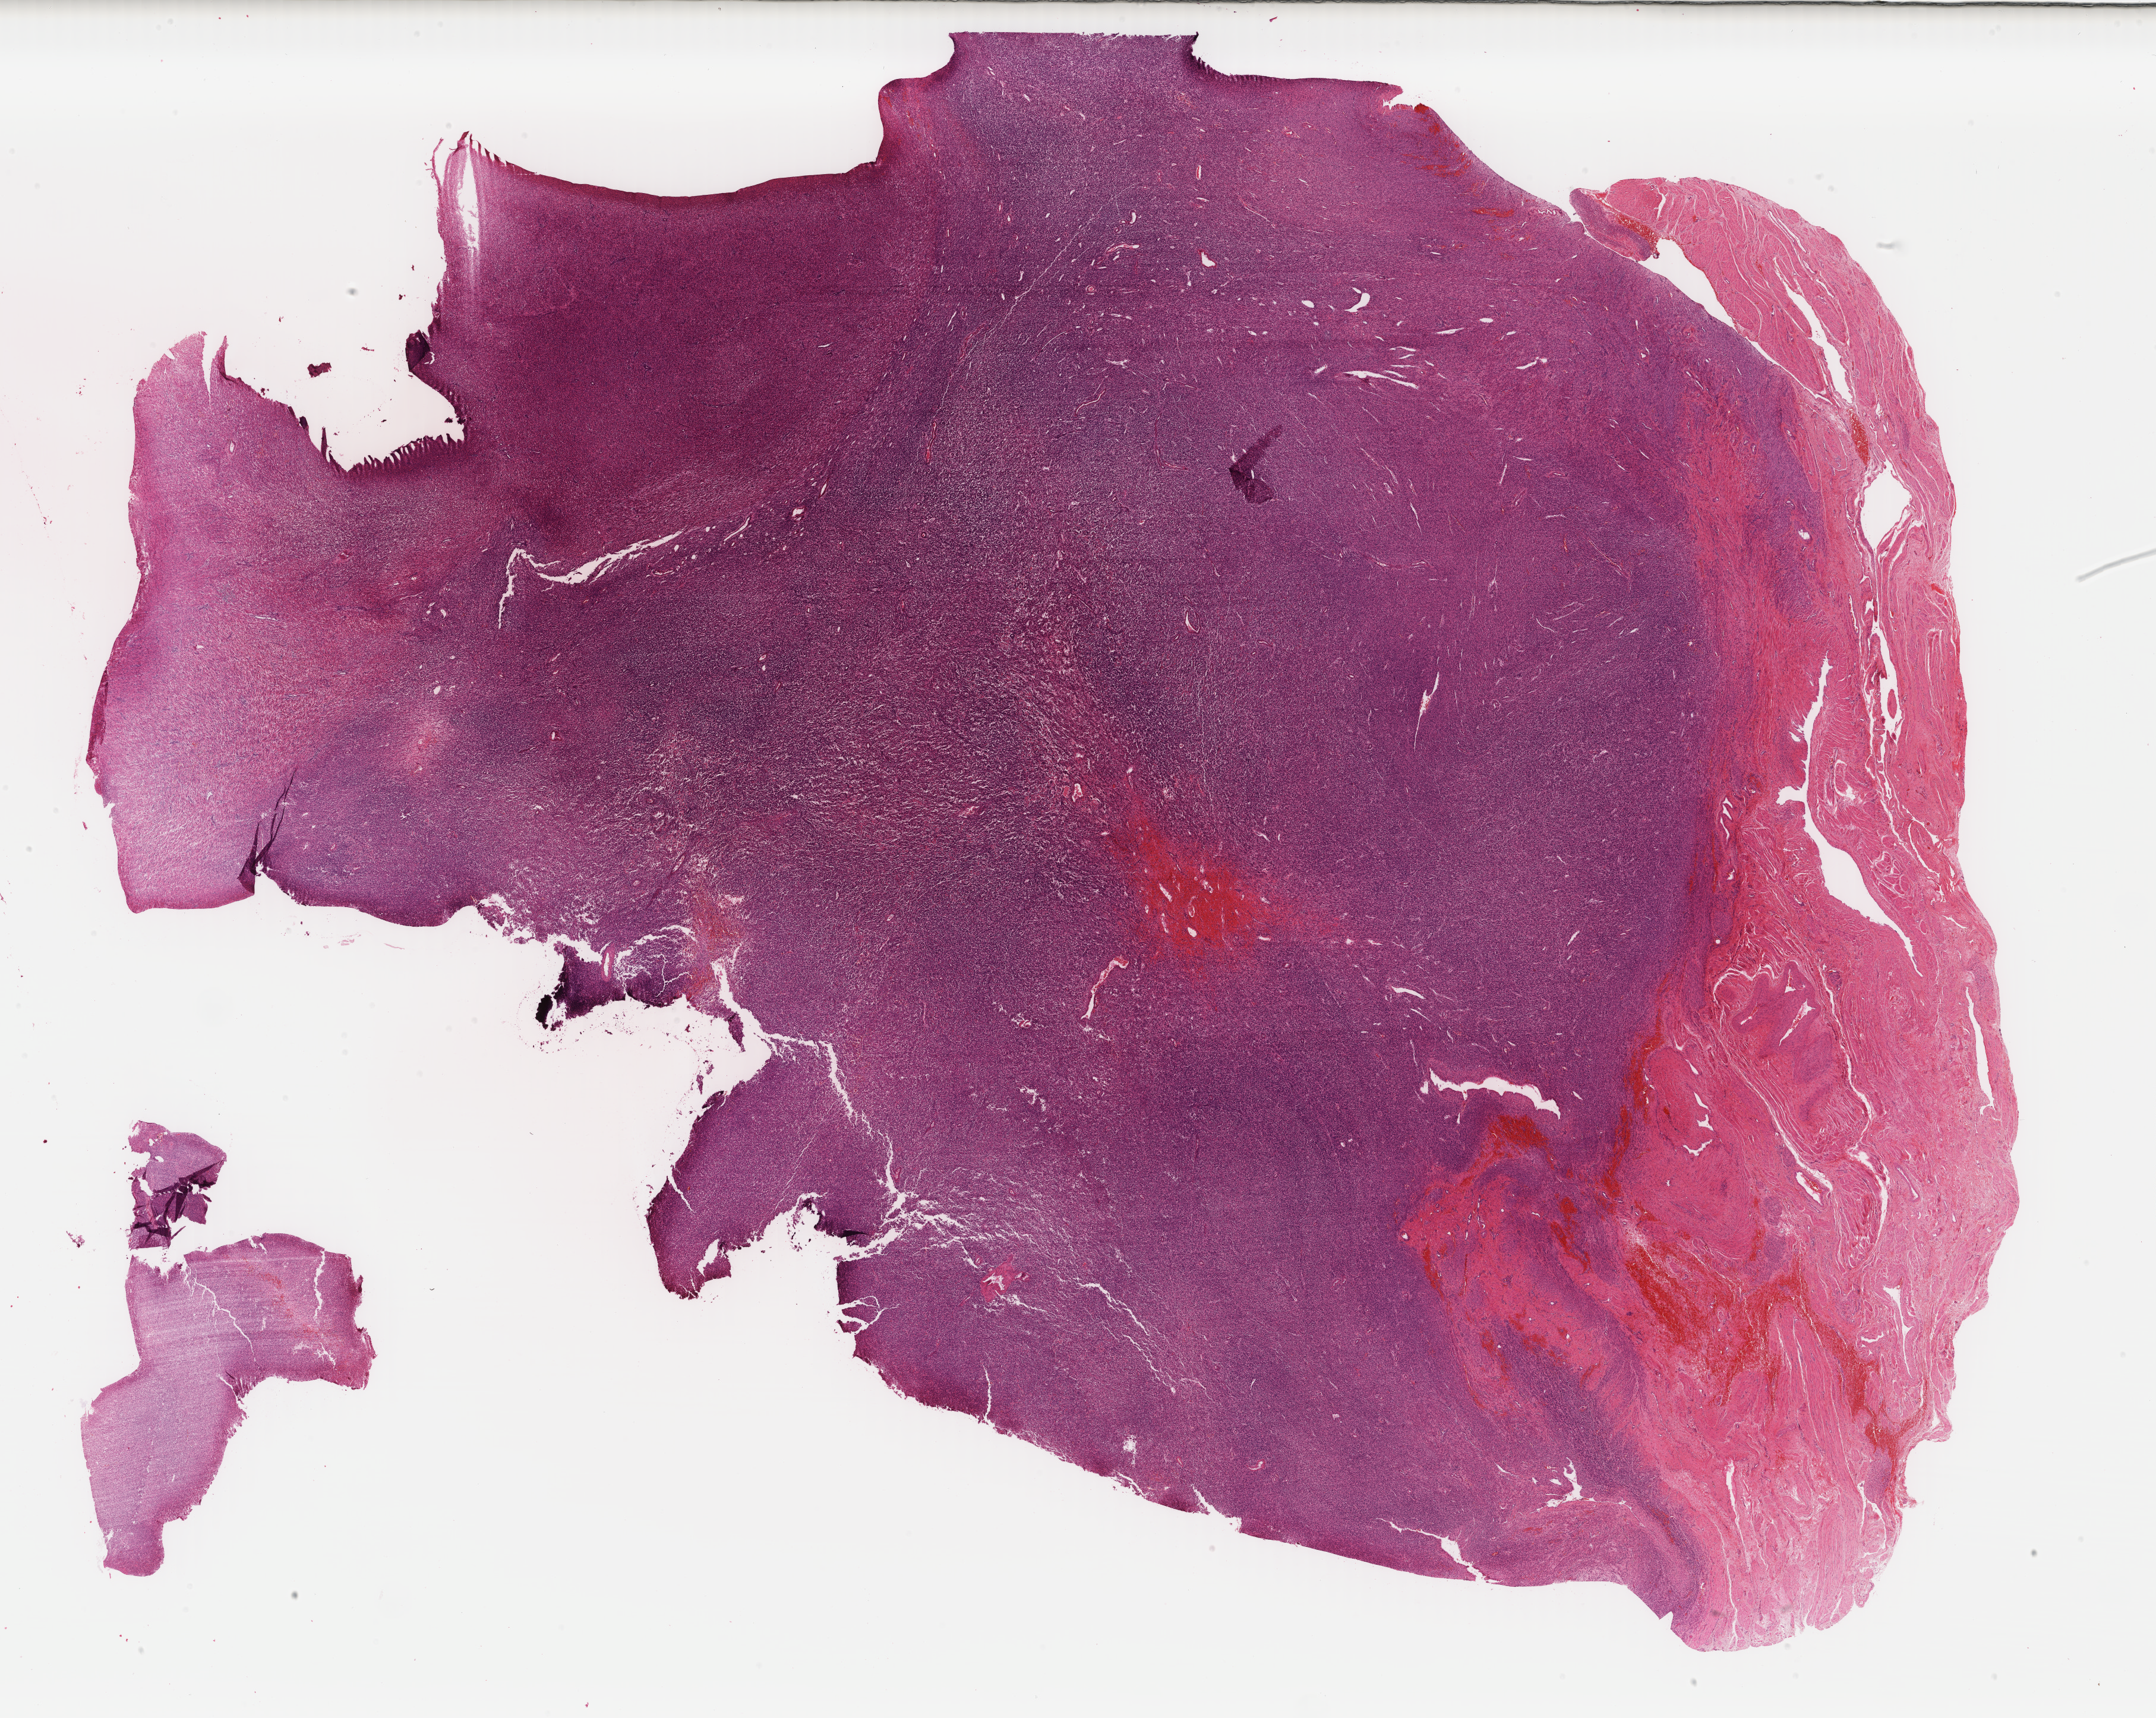
H&E-stained whole-slide image, low-resolution overview of the scanned area, about 28.8 x 23.0 mm (slide scanned at 40x); formalin-fixed paraffin-embedded (FFPE) diagnostic section; sample: primary tumour, uterus. Female patient; age at initial diagnosis 48 years.
Histologic diagnosis: Leiomyosarcoma, NOS.